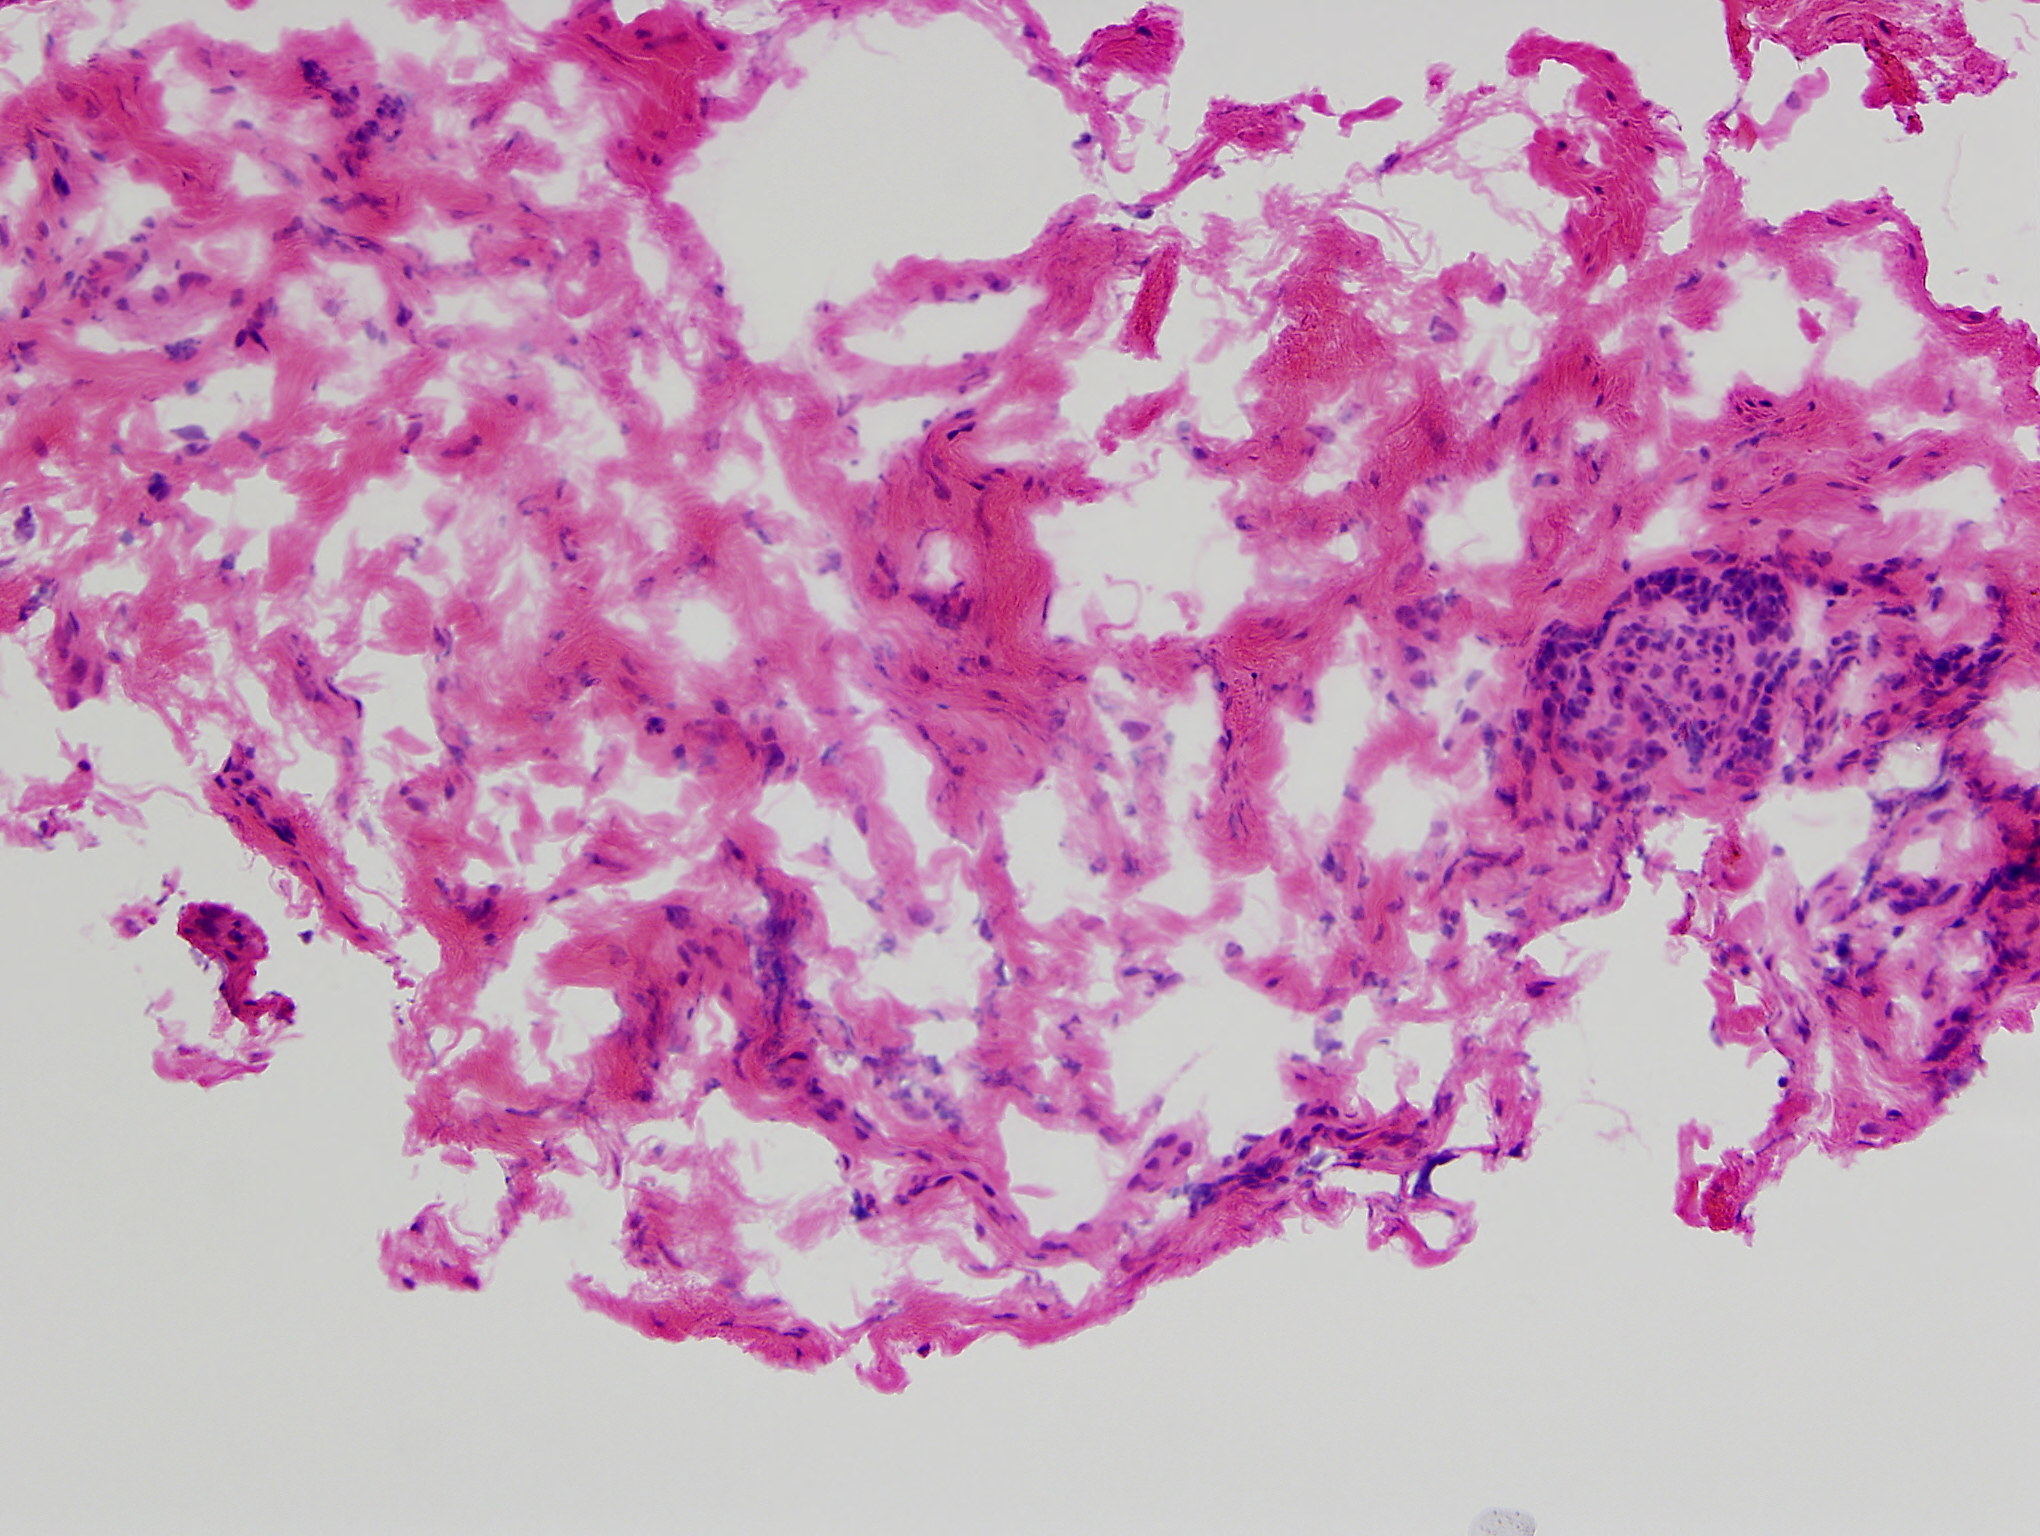
Single-field Hematoxylin and eosin (H&E) stained photomicrograph — covering about 1.0 x 0.8 mm, frozen section, sample: solid tissue normal (non-tumour tissue), head and neck. Male patient; age at initial diagnosis 56 years.
This section: solid tissue normal sample (biorepository sample class). Patient diagnosis: Squamous cell carcinoma, NOS (larynx, NOS).